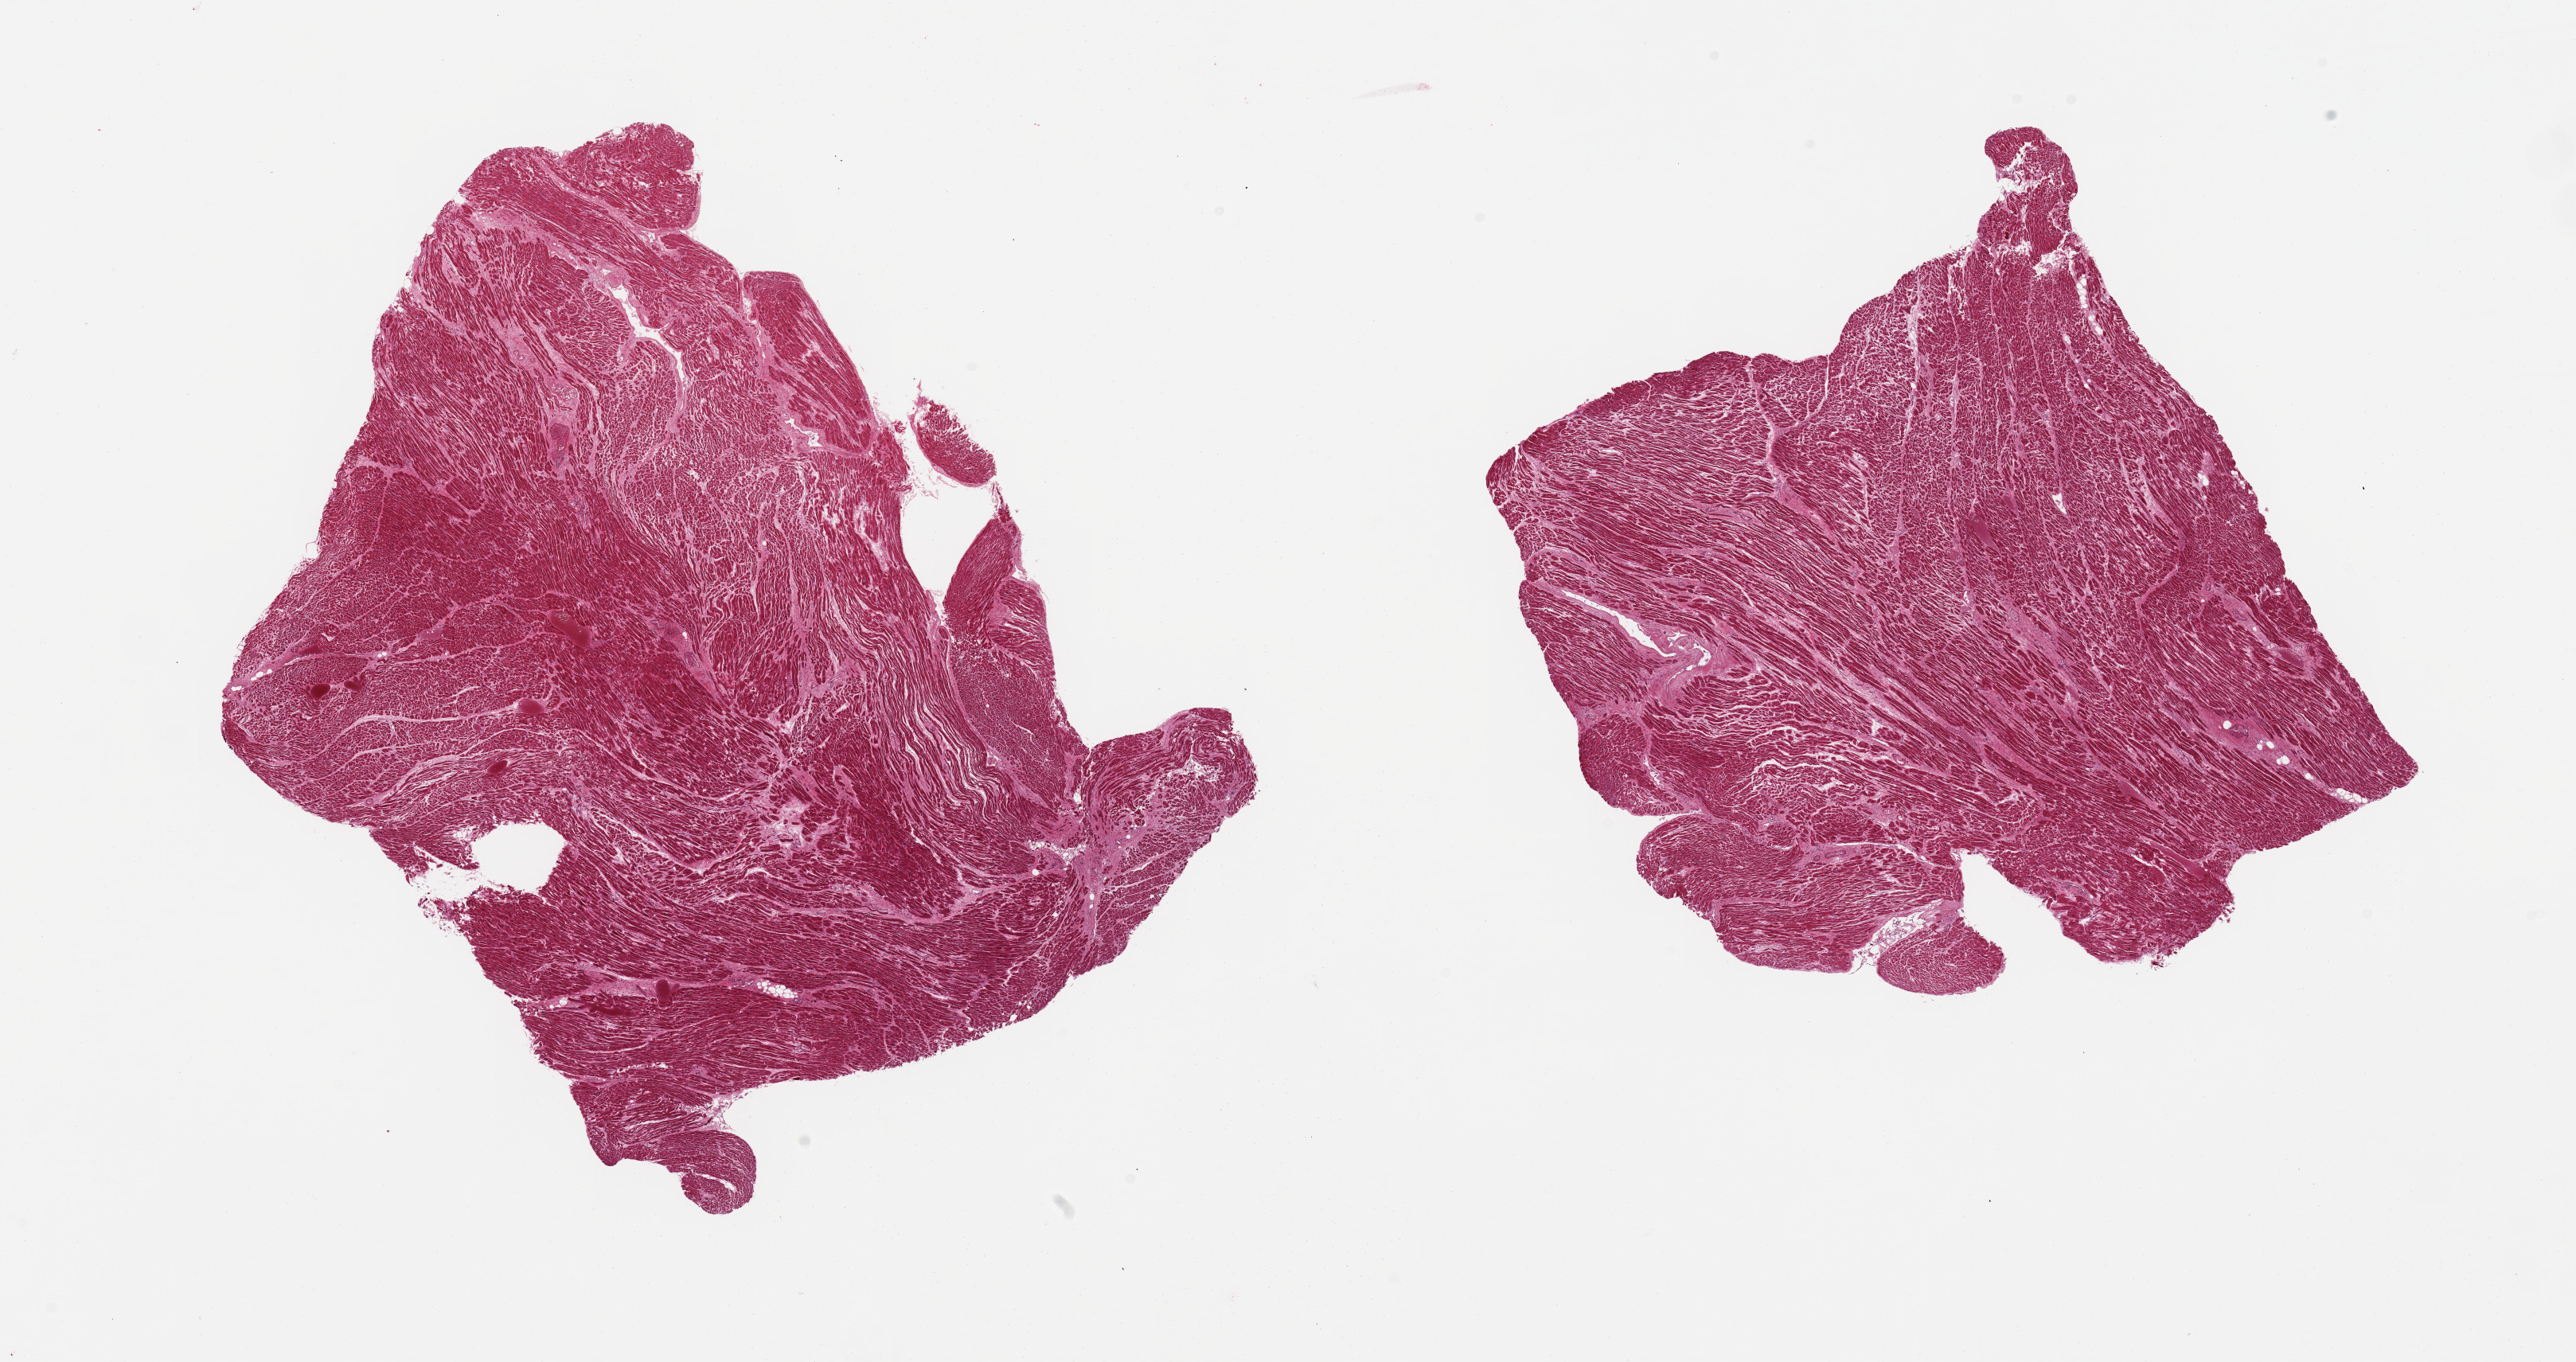
Whole-slide image, haematoxylin and eosin stain, a low-resolution overview of the entire scanned area, about 25.6 x 13.5 mm, PAXgene-fixed, paraffin-embedded tissue, sampled site (target tissue): heart, donor tissue sample. Donor: male.
Pathologist's review note for this sample: 2 pieces; some interstitial fibrosis.